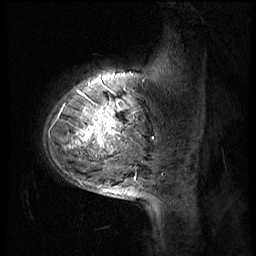
Breast MRI (dynamic contrast-enhanced), one sagittal slice. Position 11 of 56 along the scan axis. 4 images stored at this slice position (order not interpretable as contrast timing). 1.5 T. TE 4.2 ms, TR 8.9 ms. 2.5 mm slice thickness. 256 × 256 image matrix. Female patient, age 51 years. From the clinical record (not read from this slice): setting: breast cancer imaged before/during neoadjuvant chemotherapy; receptor status: triple-negative.
Structures marked on this image (semi-automatic segmentation, software-assisted and operator-edited):
- analysis volume of interest (the breast-tissue region the enhancement analysis was run in; not a lesion): bounding box <42,70,150,173> (left, top, right, bottom; pixels)
- tumour enhancement mask (voxels above the 140 % enhancement threshold inside the analysis volume of interest): <69,108,128,149>